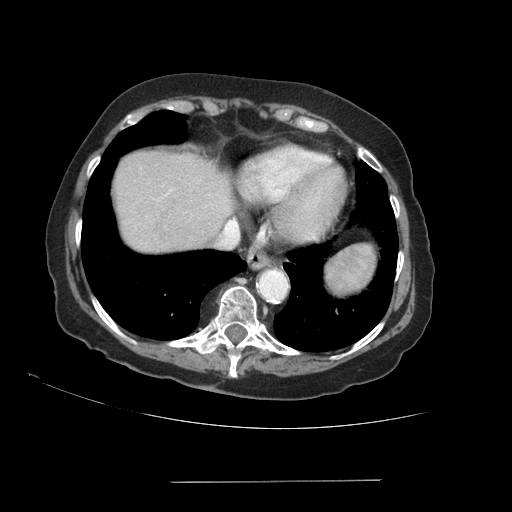
Contrast-enhanced abdominal CT (liver protocol), one axial slice. Slice 79 of 89 in the series (ordered by position). Reconstruction kernel STANDARD. 140 kVp. Soft-tissue window (W 400 / L 40 HU). 512 × 512 image matrix, field of view 400 × 400 mm. From the clinical record (not read from this slice): diagnosis: hepatocellular carcinoma (patient treated with transarterial chemoembolisation; whether this scan precedes or follows treatment is not stated here); TNM stage (as recorded): Stage-IVA; Child-Pugh class: A.
Annotated regions visible in this slice (semi-automatic segmentation, software-assisted and operator-edited):
- liver parenchyma outside the tumour (the mass and vessels are separate outlines, so this box may not span the whole liver): bounding box <112,150,232,252> (left, top, right, bottom; pixels)